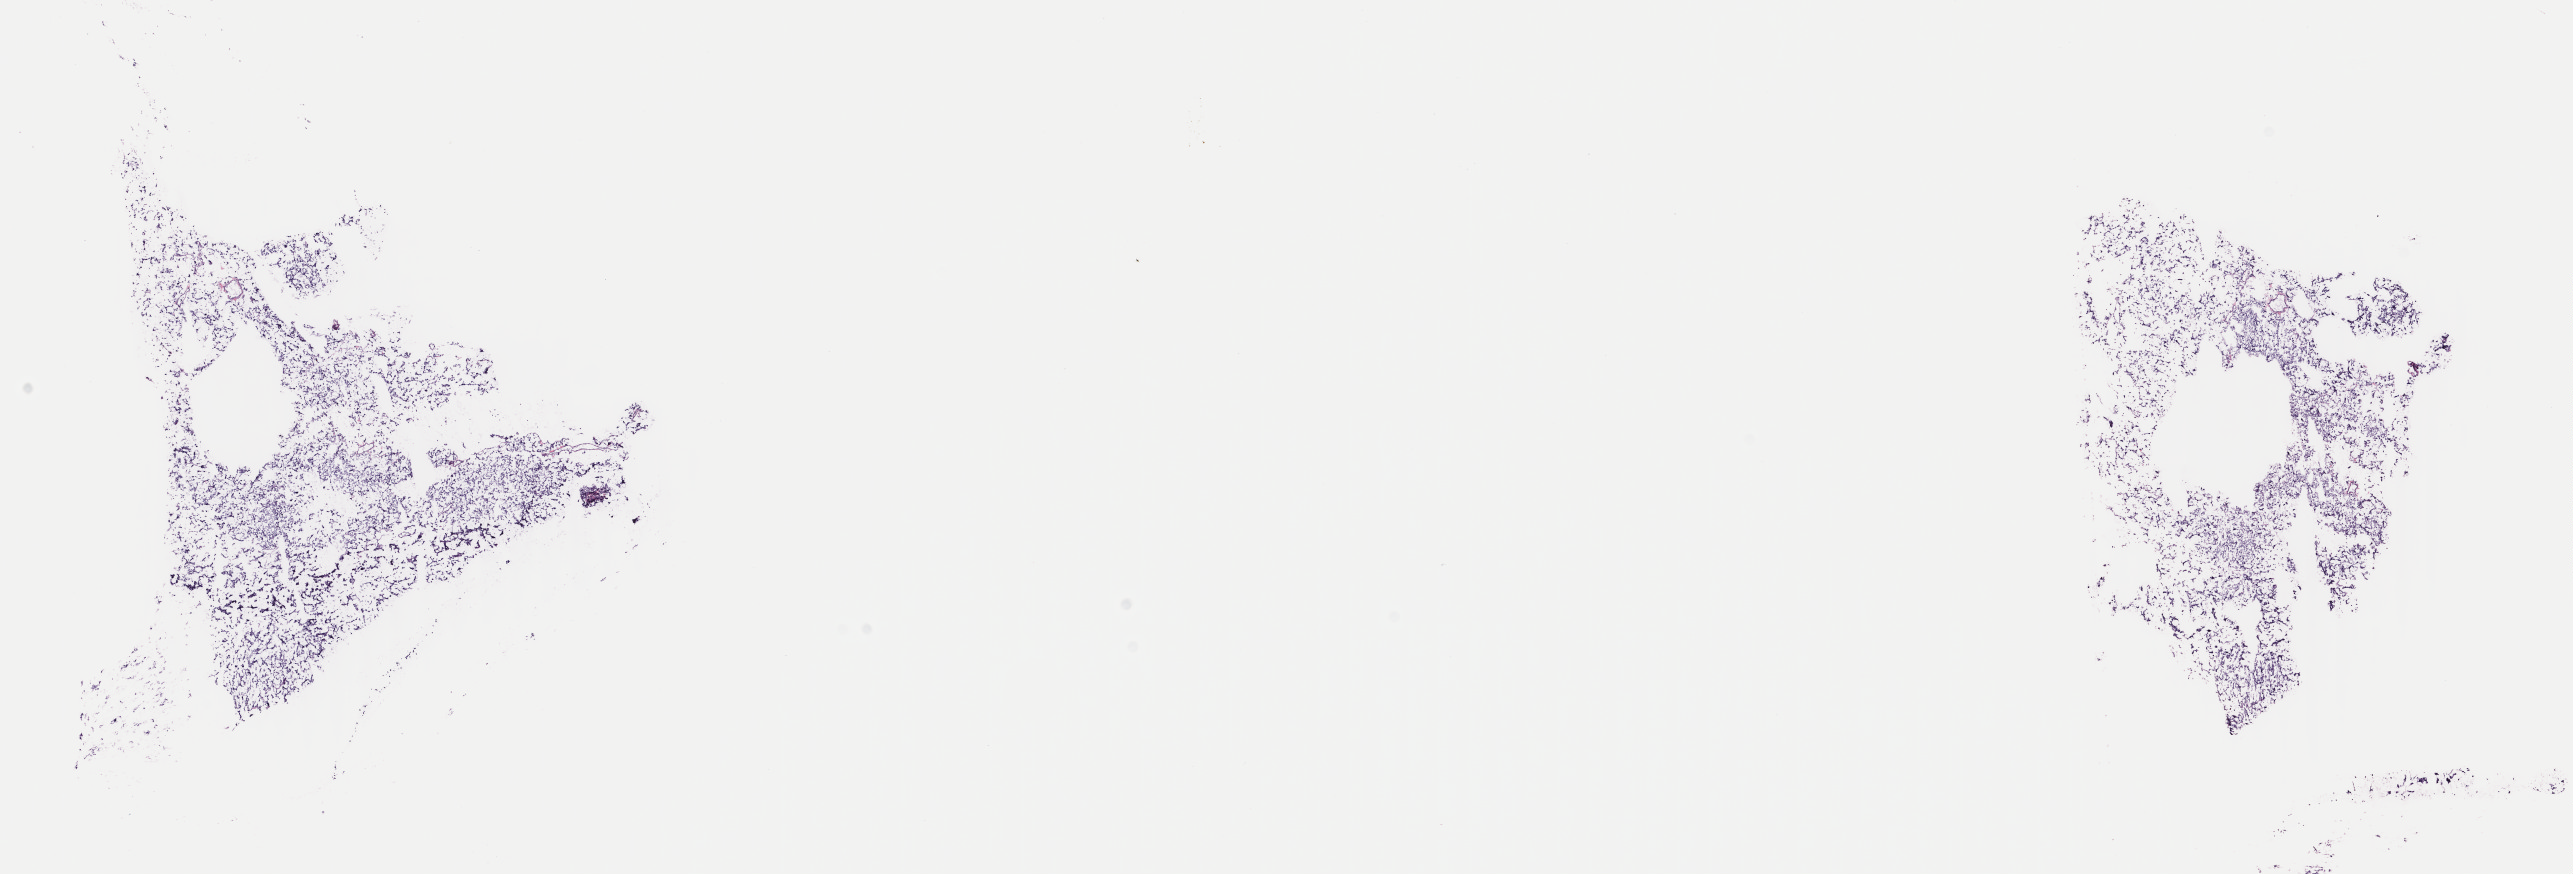
Whole-slide histology image, H&E — shown as a low-resolution overview of the whole scanned area (about 20.5 x 7.0 mm, from a 40x scan). Frozen section from the top of the tissue portion. Primary tumour sample from the adrenal gland. Female patient; age at initial diagnosis 37 years. Composition of this section per pathologist review: tumour cells 100%, tumour nuclei 80%, normal cells 0%, stromal cells 0%, necrosis 0%. Infiltration values recorded for this section: lymphocyte infiltration 1%, monocyte infiltration 0%, neutrophil infiltration 0%.
• histologic diagnosis: Pheochromocytoma, malignant
• laterality: right